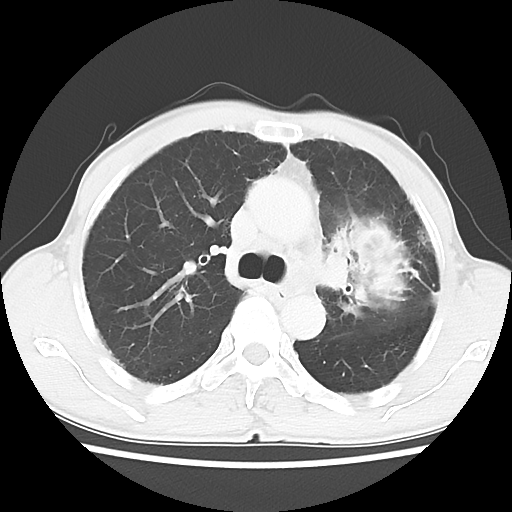
Chest CT, one axial slice; reconstruction kernel LUNG; lung window (W 1500 / L -600 HU); 5 mm slice thickness; 512 × 512 image matrix, field of view 308 × 308 mm. Patient: male, 64 years. Case-level facts recorded for this patient, not image findings: clinical TNM (as recorded): T3 N3 M0; histopathological grade: G3.
Outlined on this slice (rectangle marked by the reading radiologist):
- lung tumour (recorded histology: adenocarcinoma): bounding box [x1, y1, x2, y2] px = [325, 200, 413, 330]